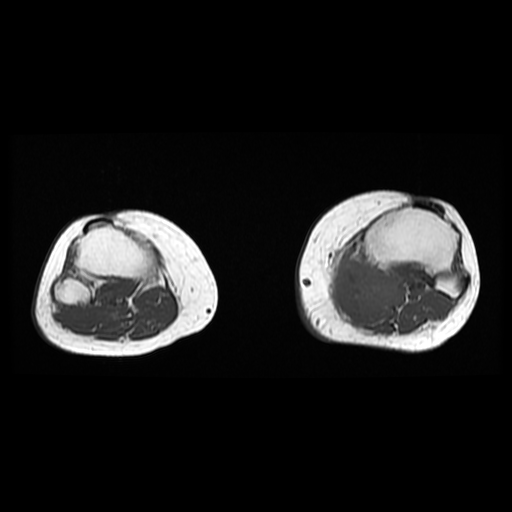
MRI of an extremity soft-tissue mass, one axial slice. Position 23 of 38 along the scan axis. 6 mm slice thickness. 512 × 512 image matrix, field of view 330 × 330 mm. Female patient. Case-level facts recorded for this patient, not image findings: histological type: extraskeletal high grade osteogenic sarcoma; grade: high; site of the primary tumour: left calf.
Annotated regions visible in this slice (outlined manually by an expert reader):
- gross tumour volume (mass): box from (x=326, y=256) to (x=405, y=315) px